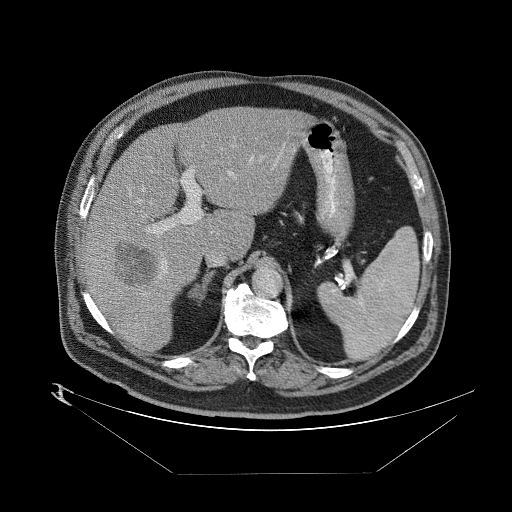
Contrast-enhanced abdominal CT (liver protocol), one axial slice. Slice 52 of 89 in the series (ordered by position). Reconstruction kernel STANDARD. One of 2 acquisitions stored at this slice position. Soft-tissue window (W 400 / L 40 HU). 512 × 512 image matrix, field of view 480 × 480 mm. Case-level facts recorded for this patient, not image findings: diagnosis: hepatocellular carcinoma (patient treated with transarterial chemoembolisation; whether this scan precedes or follows treatment is not stated here); TNM stage (as recorded): Stage-II; Child-Pugh class: B; tumour differentiation: moderately differentiated; tumour nodularity: multinodular.
Annotated regions visible in this slice (semi-automatic segmentation, software-assisted and operator-edited):
- abdominal aorta: bounding box <252,267,282,297> (left, top, right, bottom; pixels)
- liver parenchyma outside the tumour (the mass and vessels are separate outlines, so this box may not span the whole liver): <78,104,306,352>
- mass: <110,236,156,285>
- liver vessels: <89,155,261,333>